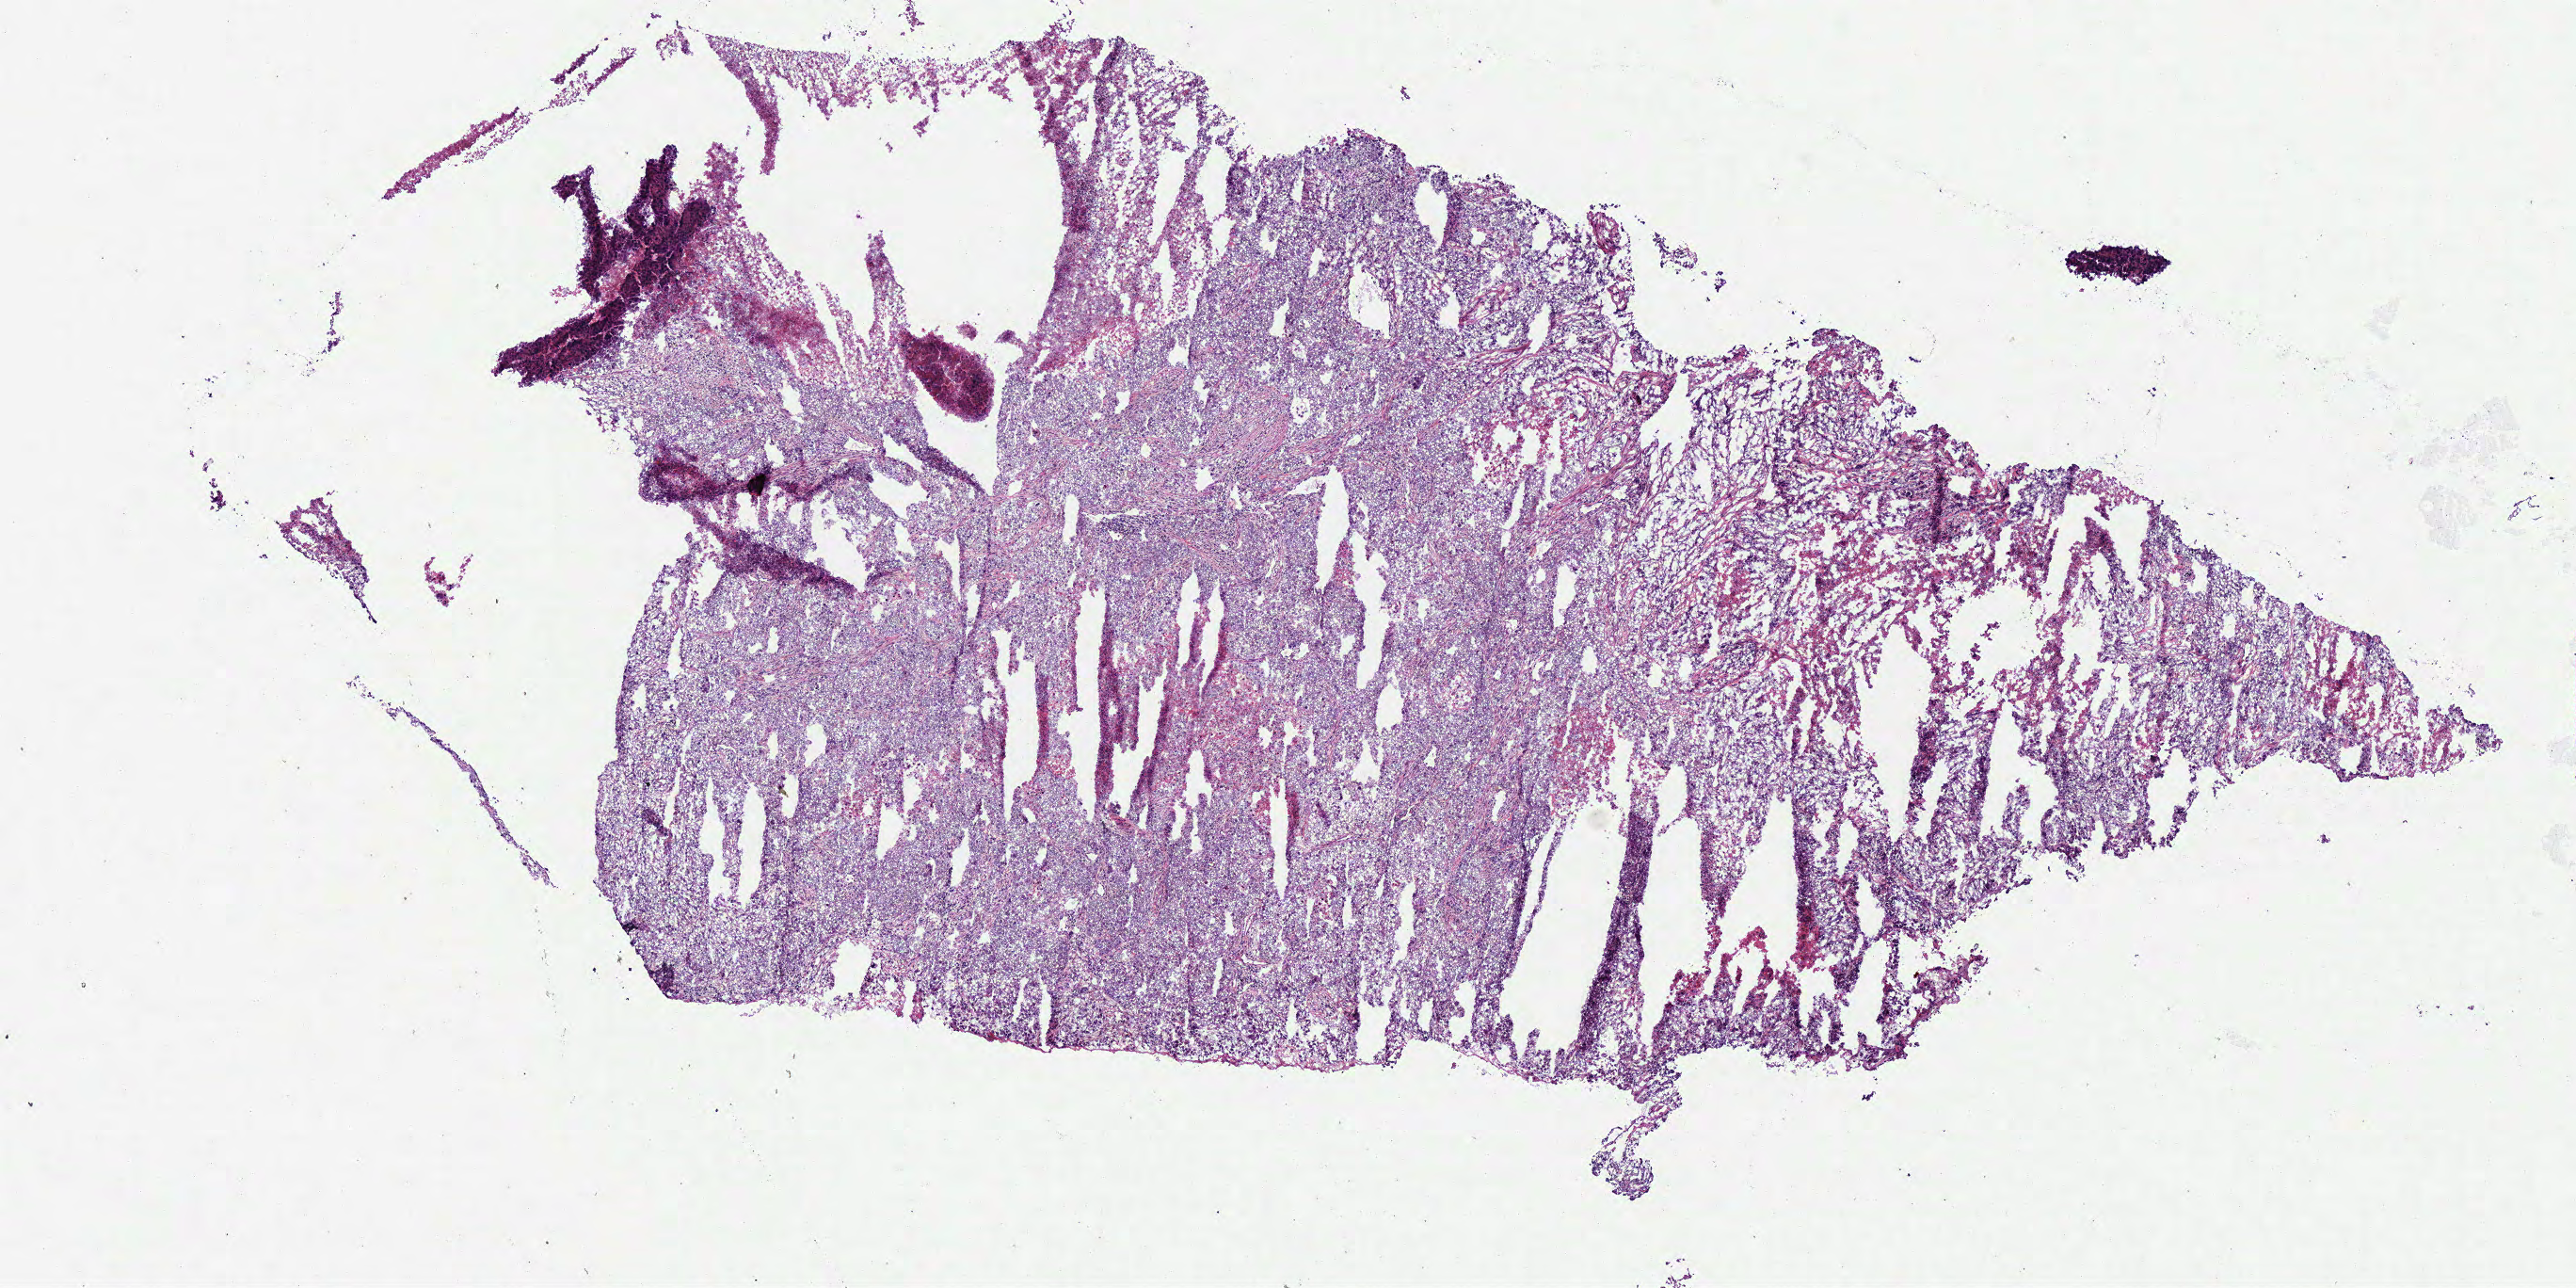
Whole-slide histology image, H&E, shown as a low-resolution overview of the whole scanned area (about 10.8 x 5.4 mm), frozen section, lung, primary tumour sample. Female patient; age at initial diagnosis 81 years. Pathologist review of this section (percent, as recorded): tumour cells 65%, tumour nuclei 85%, normal cells 0%, stromal cells 10%, necrosis 25%.
• pathologic diagnosis: Clear cell adenocarcinoma, NOS (upper lobe, lung)
• AJCC pathologic stage: IIIA (7th edition)
• laterality: right